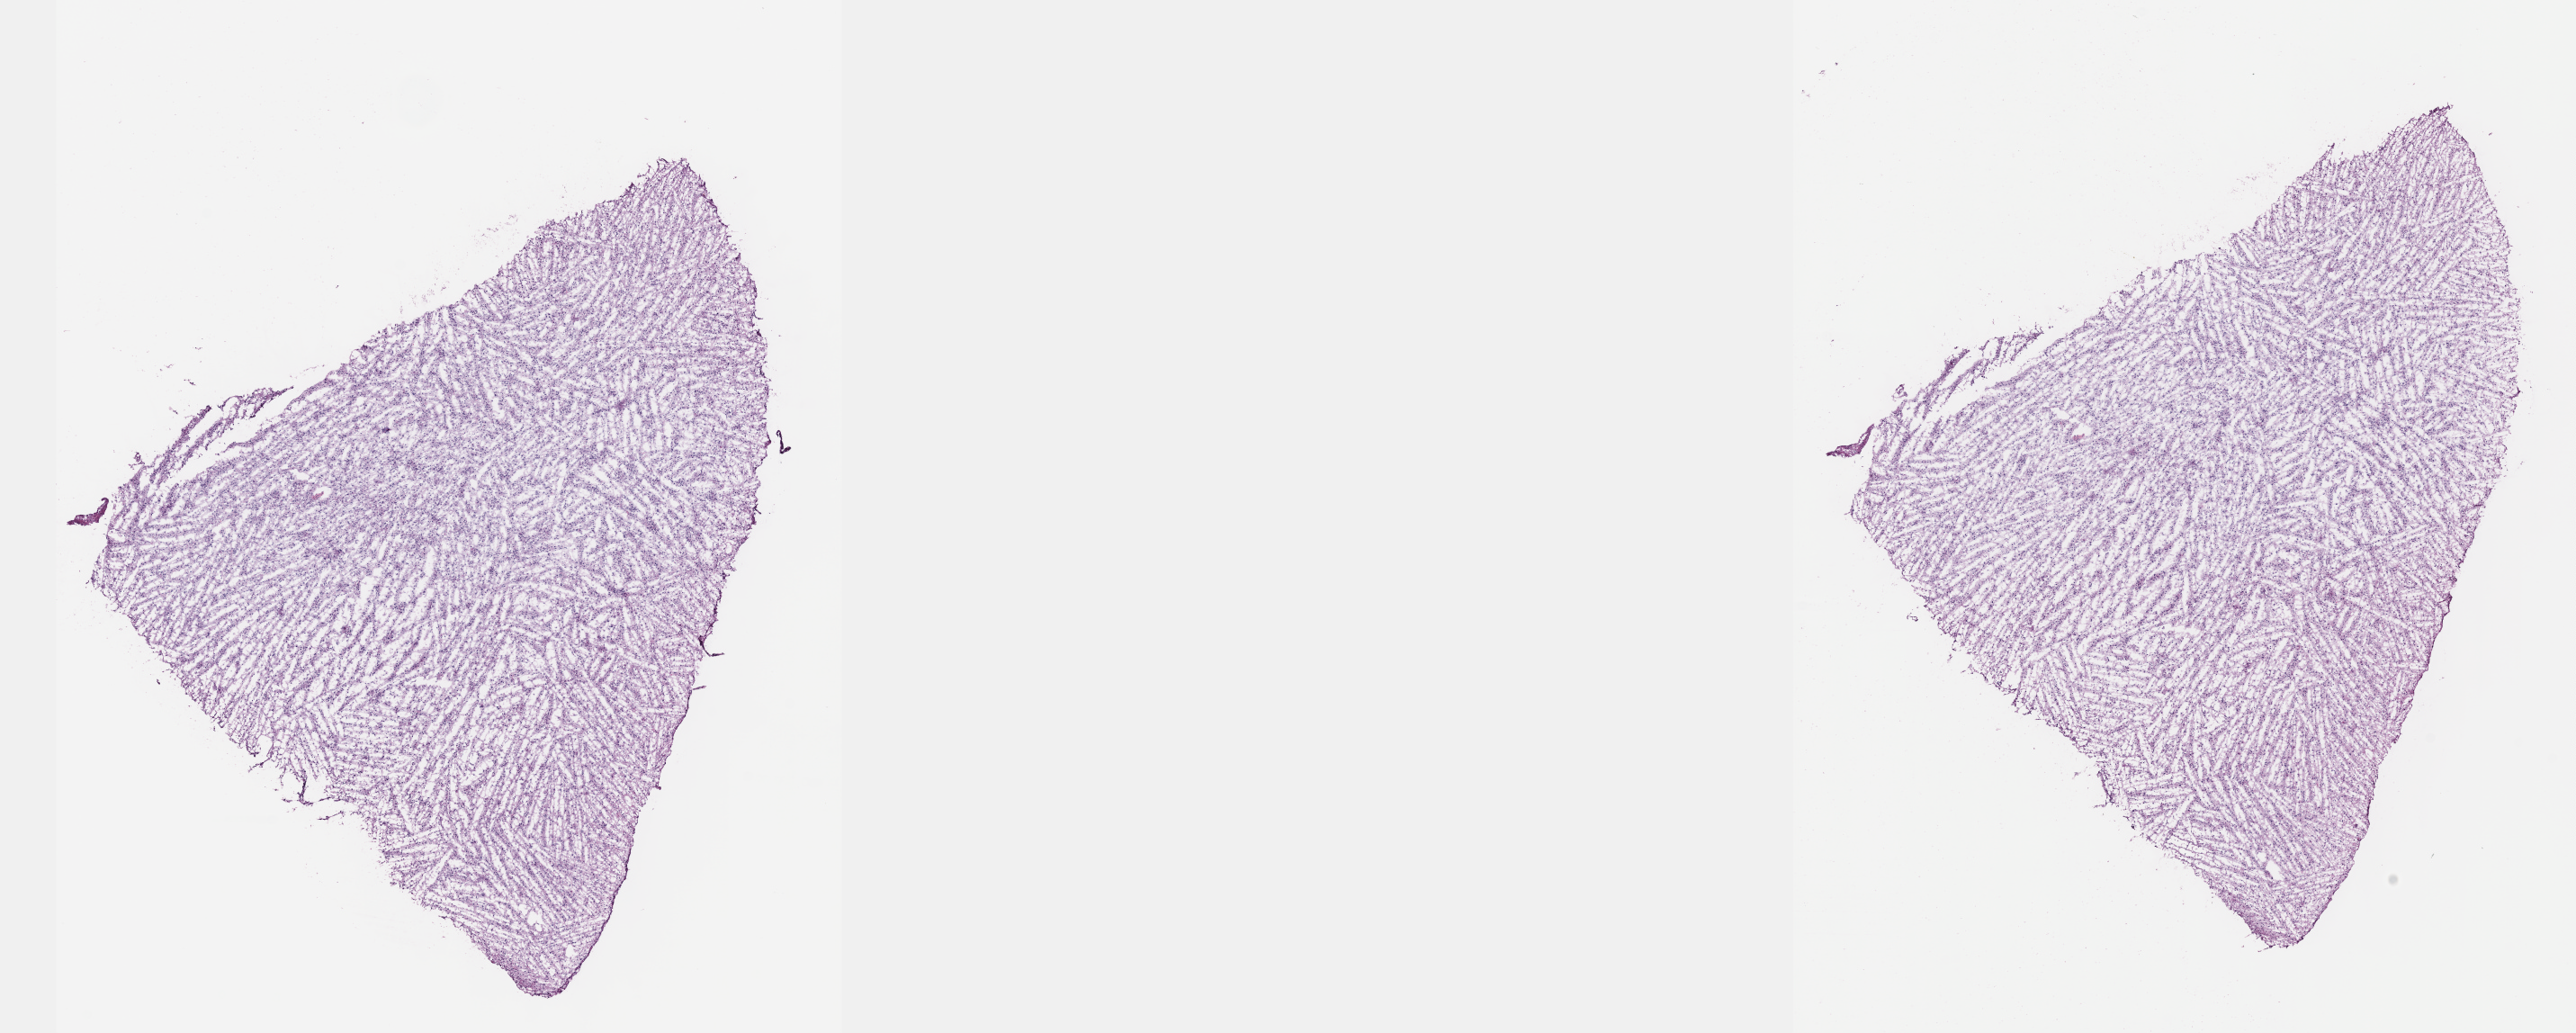
Digitized H&E tissue section (whole slide), low-resolution overview of the scanned area, about 23.1 x 9.3 mm; frozen section; primary tumour sample from the brain. Male patient; age at initial diagnosis 29 years. Histologic grade: G2 (moderately differentiated). Slide review estimates, as recorded: tumour cells 50%, tumour nuclei 90%, normal cells 10%, stromal cells 40%, necrosis 0%. Inflammatory infiltration, as recorded: lymphocyte infiltration 0%, monocyte infiltration 0%, neutrophil infiltration 0%.
* pathologic diagnosis: Oligodendroglioma, NOS (cerebrum)
* laterality: left